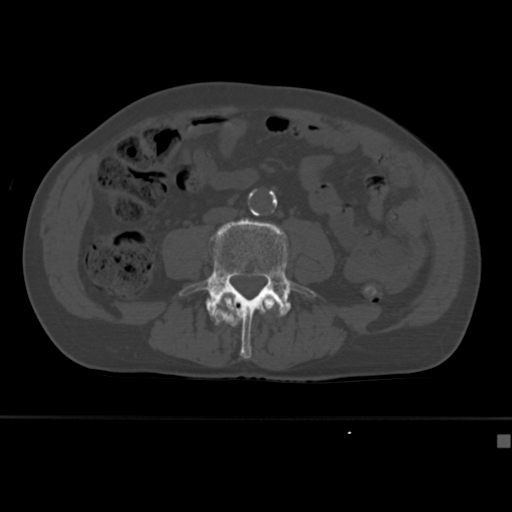
CT including the spine, one axial slice; slice 110 of 430 in the series (ordered by position); reconstruction kernel Br40s; 120 kVp; bone window (W 1800 / L 400 HU); 1.5 mm slice thickness; 512 × 512 image matrix. Male patient, age 64 years. Case-level facts recorded for this patient, not image findings: primary cancer: uterus.
Outlined on this slice (semi-automatic segmentation, software-assisted and operator-edited):
- L3 vertebra: bounding box [x1, y1, x2, y2] px = [219, 293, 276, 312]
- L4 vertebra: [179, 218, 316, 359]